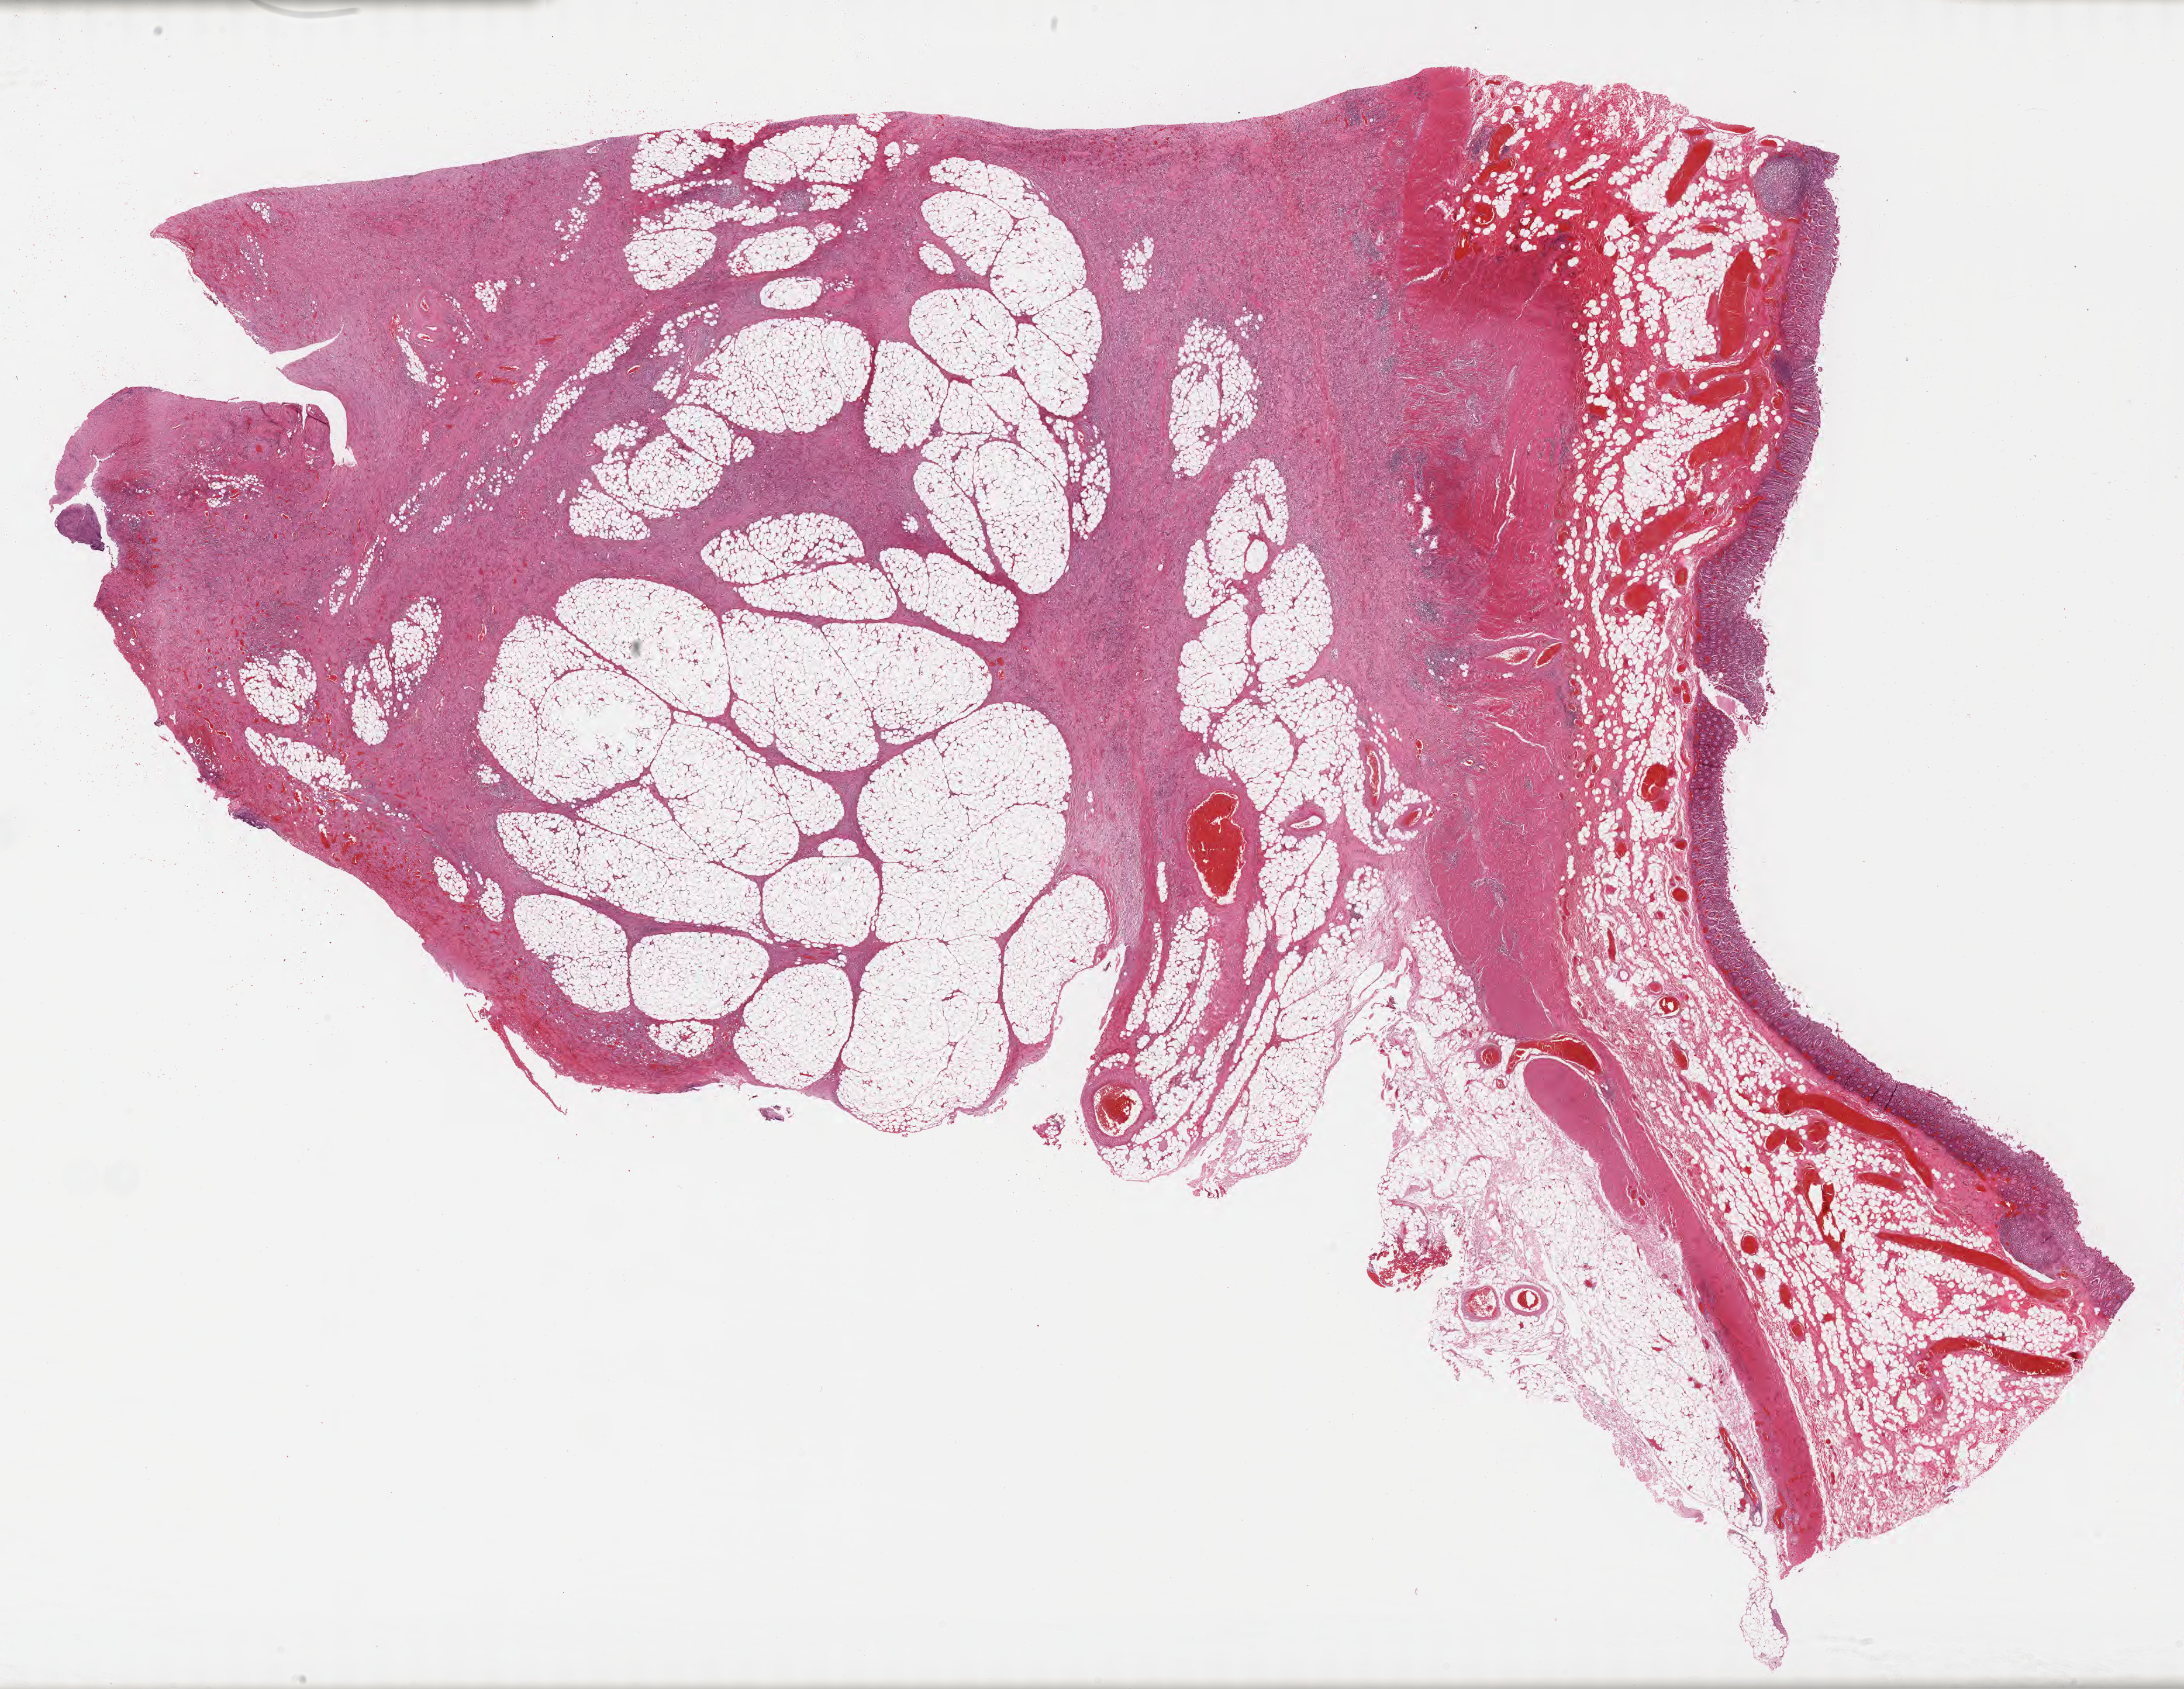
Digitized hematoxylin and eosin (H&E)-stained section, whole scanned area (about 30.2 x 23.3 mm) shown as a low-resolution overview; formalin-fixed, paraffin-embedded (FFPE) tissue; specimen: non-tumor (normal tissue) sample from a patient with burkitt lymphoma, NOS. Male patient, aged 26. Slide review estimates, as recorded: tumor cells 0%, tumor nuclei 0%, stromal cells 0%, necrosis 0%, normal cells 100%. Infiltration values recorded for this section: lymphocyte infiltration 20%, monocyte infiltration 25%, neutrophil infiltration 10%.
This section: non-tumor tissue sample; the patient's diagnosis is given above. Section: top of the tissue portion.